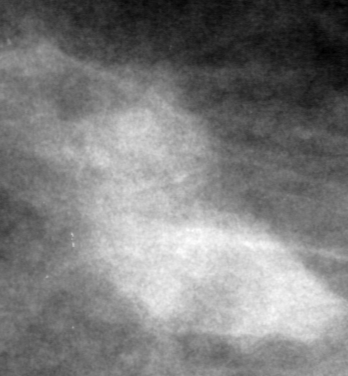
Cropped region of a digitized screen-film mammogram centred on a radiologist-marked abnormality, left breast, CC view, BI-RADS breast density category 2 (scale 1–4).
Finding: mass, shape lobulated, margins obscured; BI-RADS assessment category 0 (incomplete: needs additional imaging); pathology (as recorded): malignant.